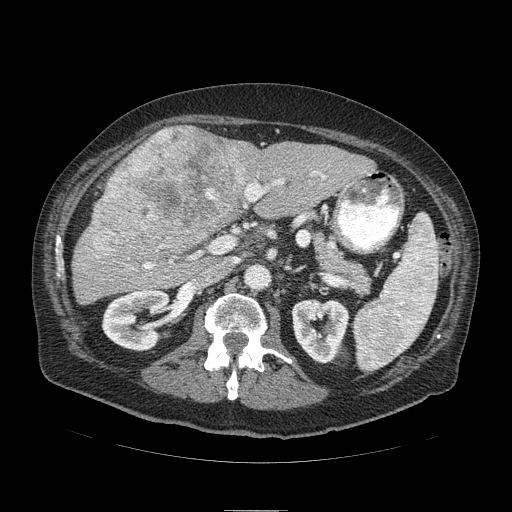
Contrast-enhanced abdominal CT (liver protocol), one axial slice. Slice 44 of 103 in the series (ordered by position). Soft-tissue window (W 400 / L 40 HU). 2.5 mm slice thickness. 512 × 512 image matrix, field of view 440 × 440 mm. From the clinical record (not read from this slice): diagnosis: hepatocellular carcinoma (patient treated with transarterial chemoembolisation; whether this scan precedes or follows treatment is not stated here); TNM stage (as recorded): Stage-IIIA; Child-Pugh class: B; tumour differentiation: well differentiated; tumour size: 13 cm.
Structures marked on this image (semi-automatic segmentation, software-assisted and operator-edited):
- liver parenchyma outside the tumour (the mass and vessels are separate outlines, so this box may not span the whole liver): box from (x=72, y=126) to (x=374, y=304) px
- mass: (x=88, y=126)–(x=255, y=259)
- liver vessels: (x=132, y=171)–(x=325, y=269)